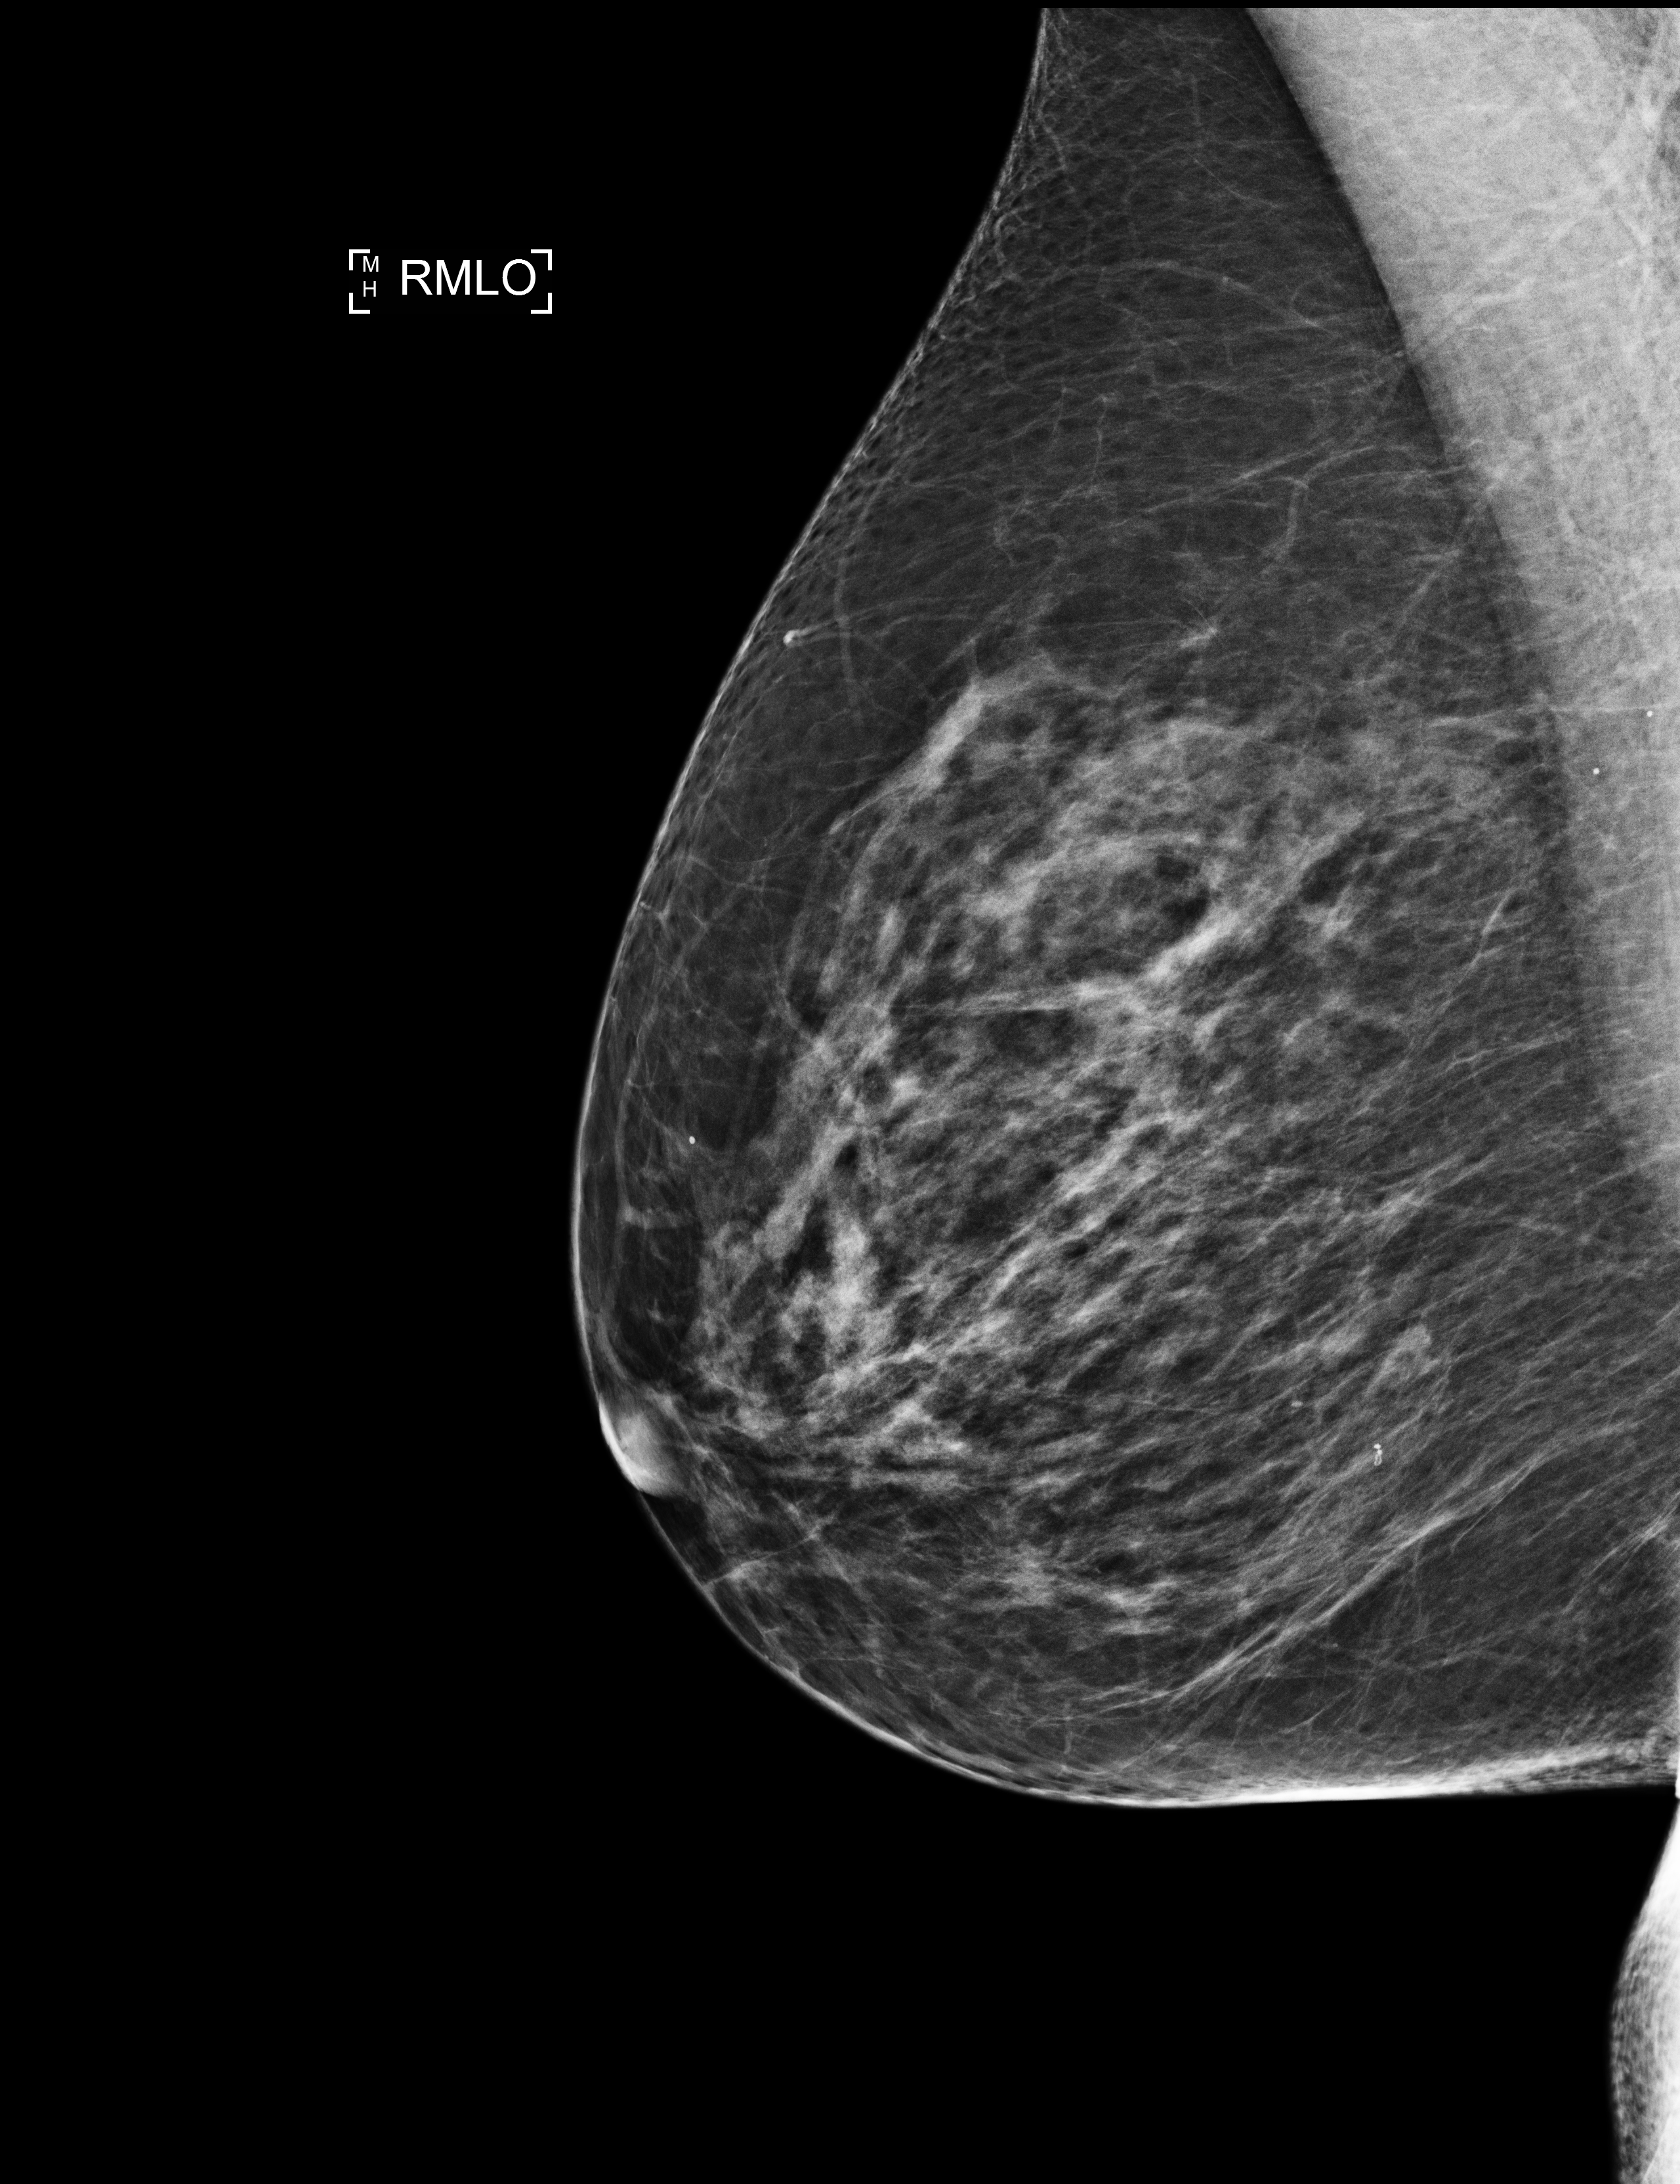
Annual screening mammography examination; system: Selenia Dimensions. Patient aged 71 years (female).
Image type: full-field digital mammogram. Breast: right. Projection: MLO view.